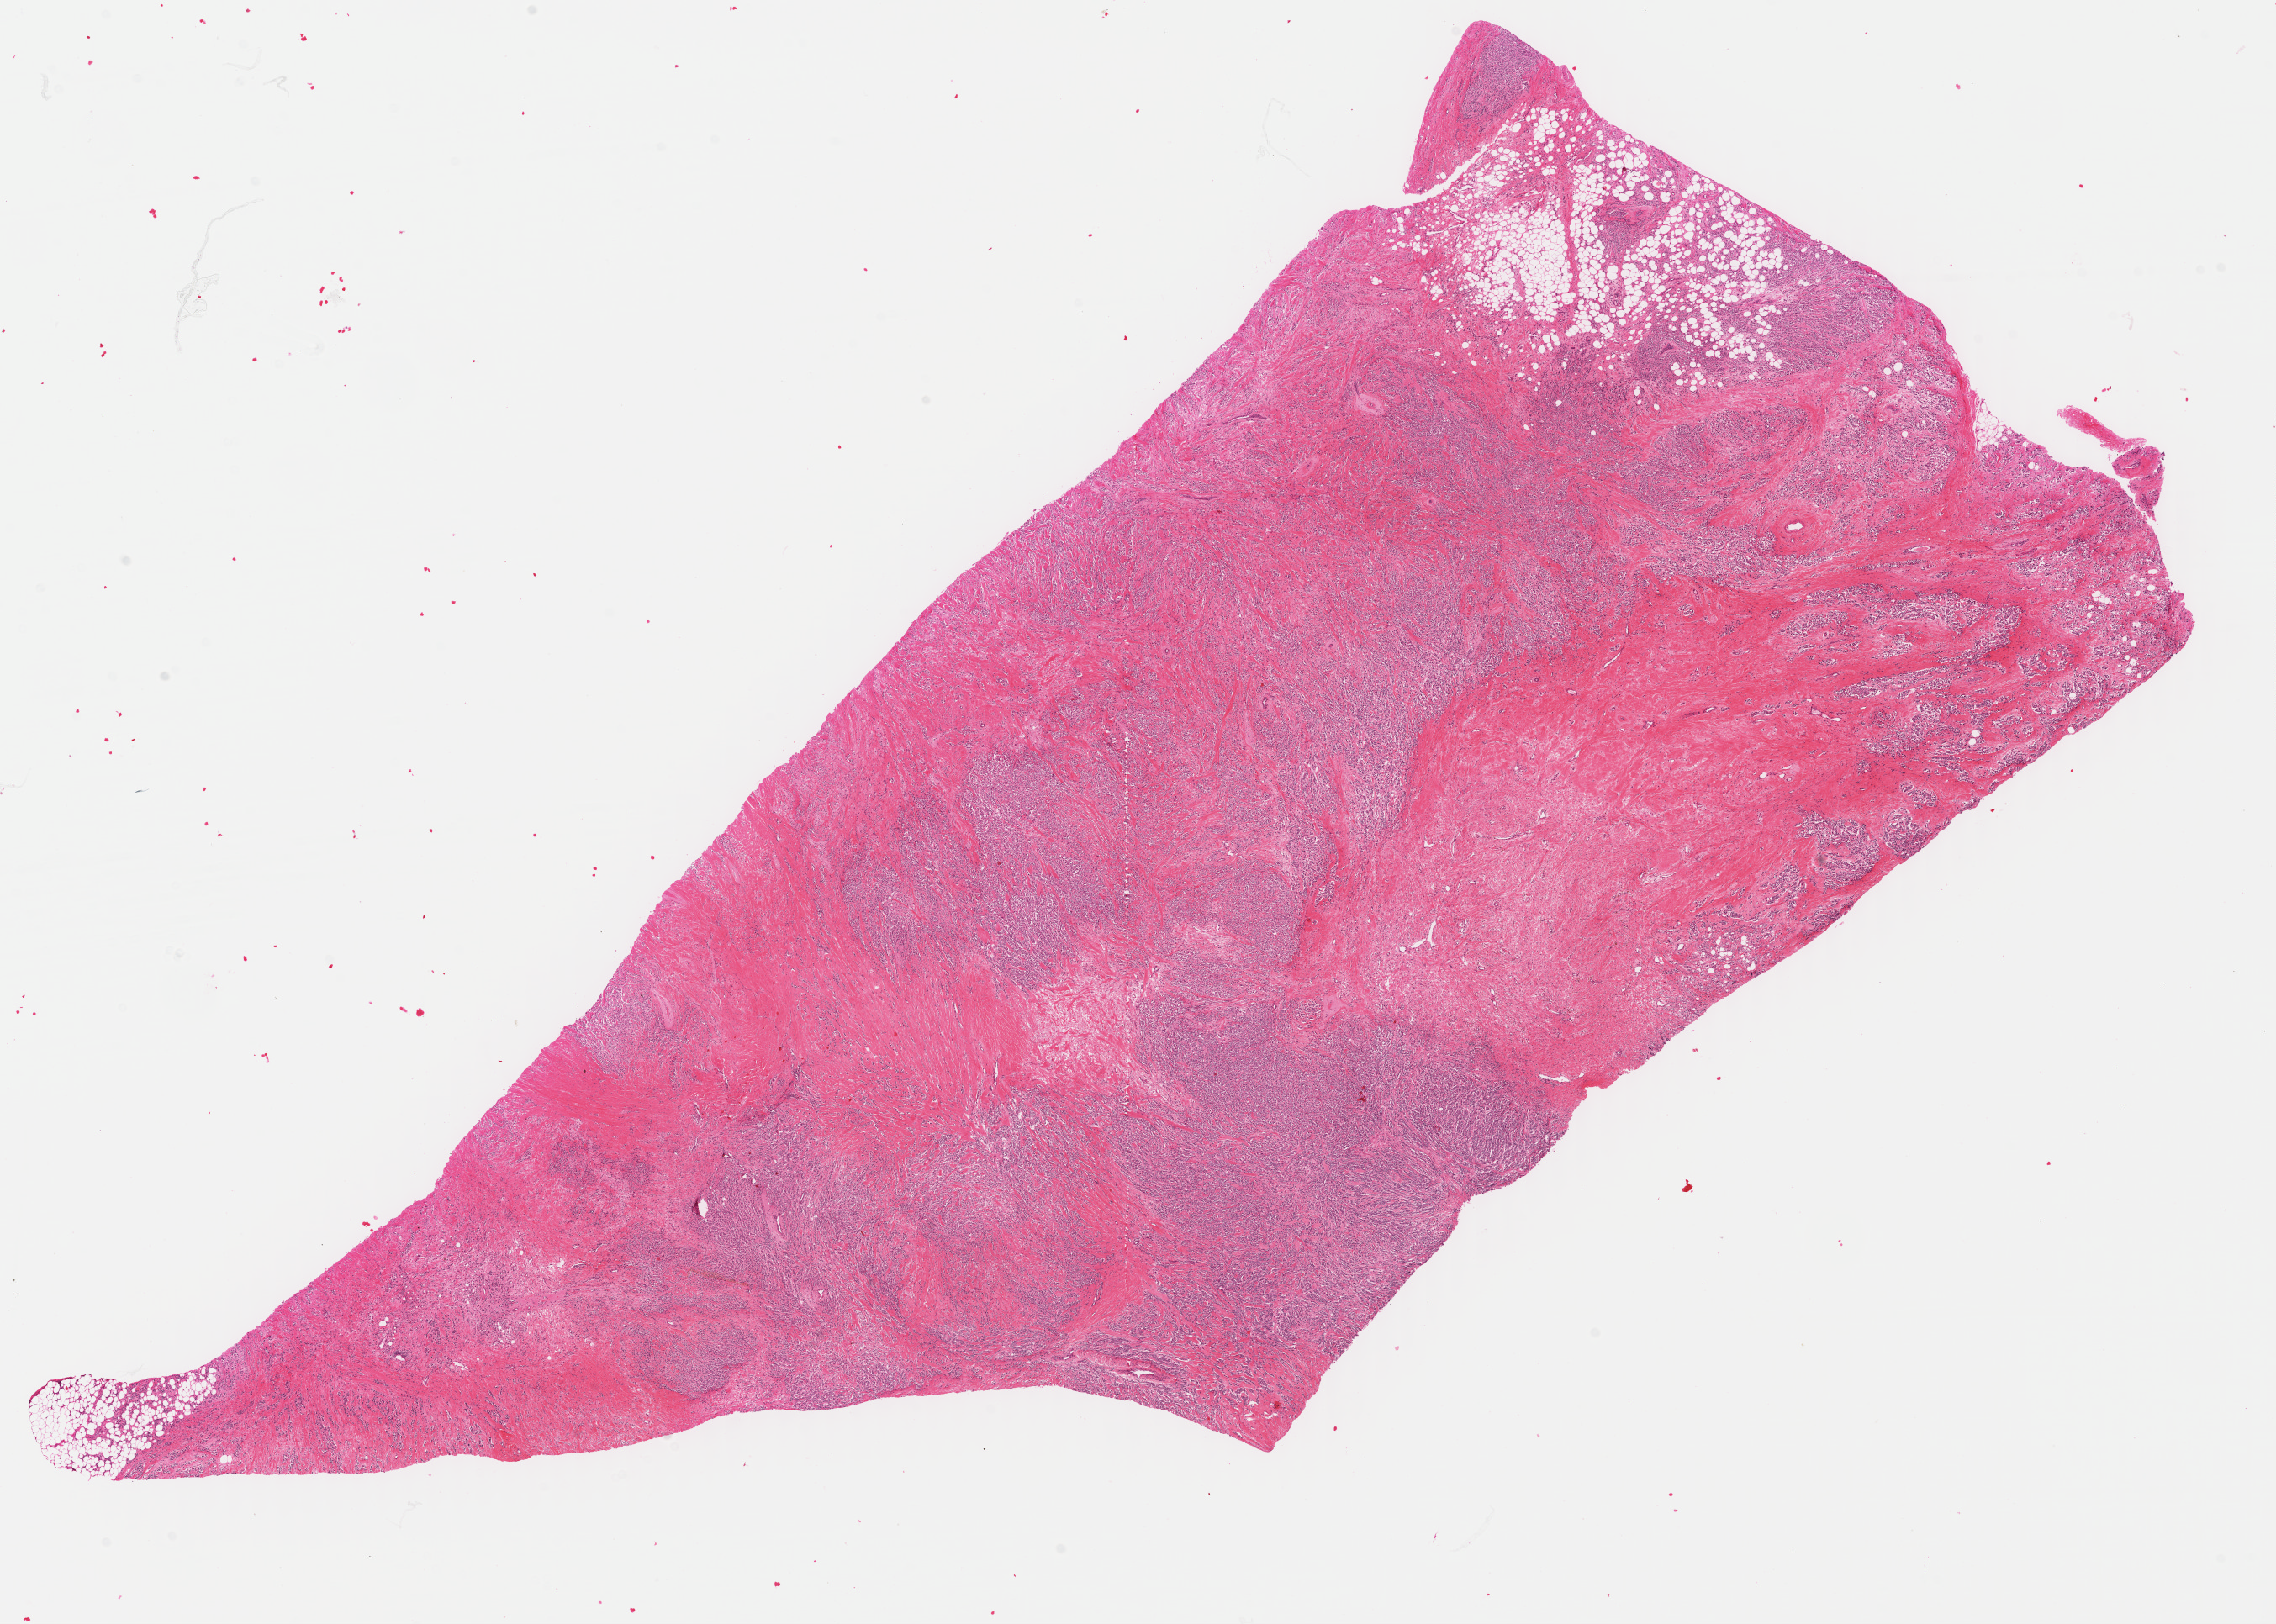
Digitized H&E-stained tissue section (whole slide) — a low-resolution overview of the entire scanned area, about 21.3 x 15.2 mm (acquisition: 40x scan); formalin-fixed paraffin-embedded (FFPE) diagnostic section; primary tumour sample from the breast. Female patient; age at initial diagnosis 64 years.
Pathologic diagnosis: Lobular carcinoma, NOS. Laterality: right. AJCC pathologic stage: IIA.